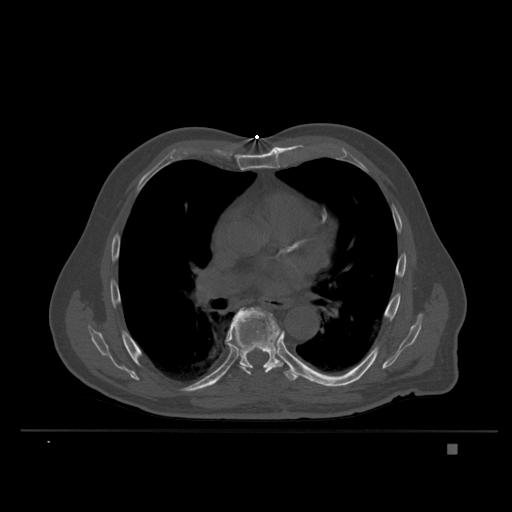
CT including the spine, one axial slice; position 237 of 435 along the scan axis; bone window (W 1800 / L 400 HU); 512 × 512 image matrix, field of view 434 × 434 mm. Patient: male, 73 years. From the clinical record (not read from this slice): primary cancer: skin.
Structures marked on this image (semi-automatic segmentation, software-assisted and operator-edited):
- T7 vertebra: box from (x=226, y=307) to (x=284, y=375) px
- T8 vertebra: (x=229, y=311)–(x=301, y=381)